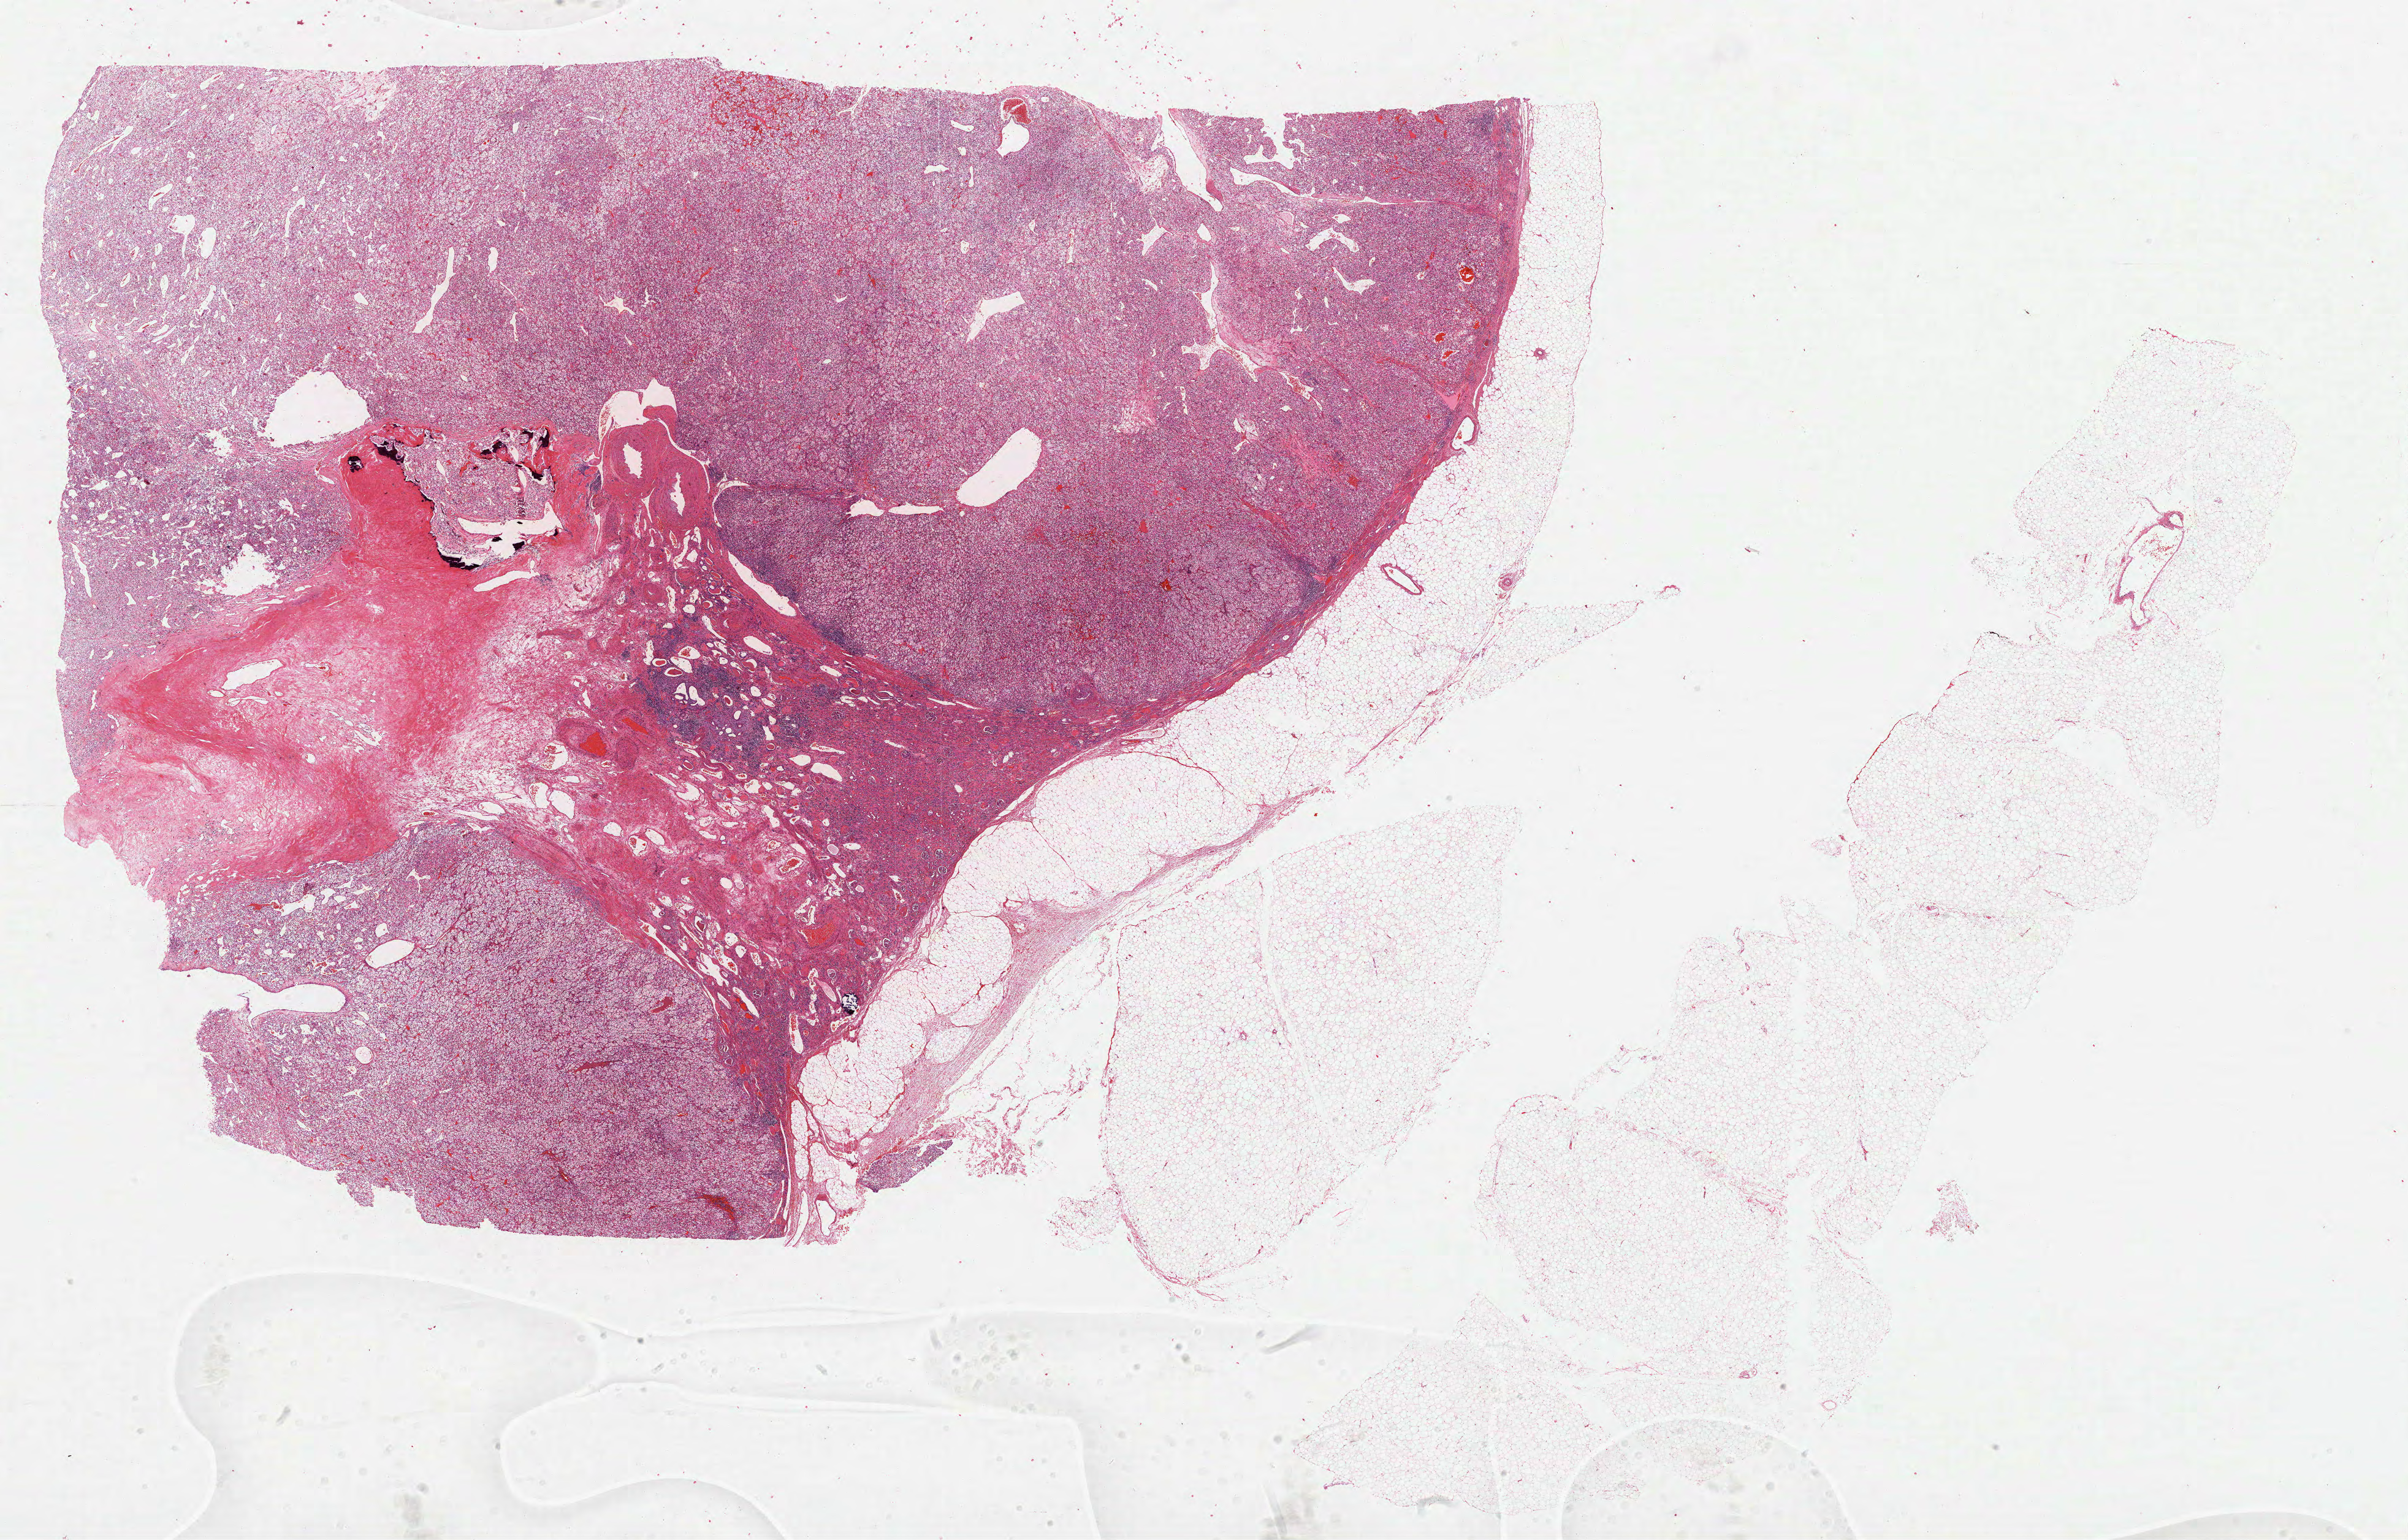
Whole-slide histology image, H&E-stained, whole scanned area (about 31.7 x 20.3 mm, acquisition: 40x scan) shown as a low-resolution overview. Formalin-fixed paraffin-embedded (FFPE) diagnostic section. Kidney, primary tumour sample. Female, age 76 years at initial diagnosis. Histologic grade: G2 (moderately differentiated).
Pathologic diagnosis: Clear cell adenocarcinoma, NOS. TNM: T3b NX M0. AJCC pathologic stage: III.